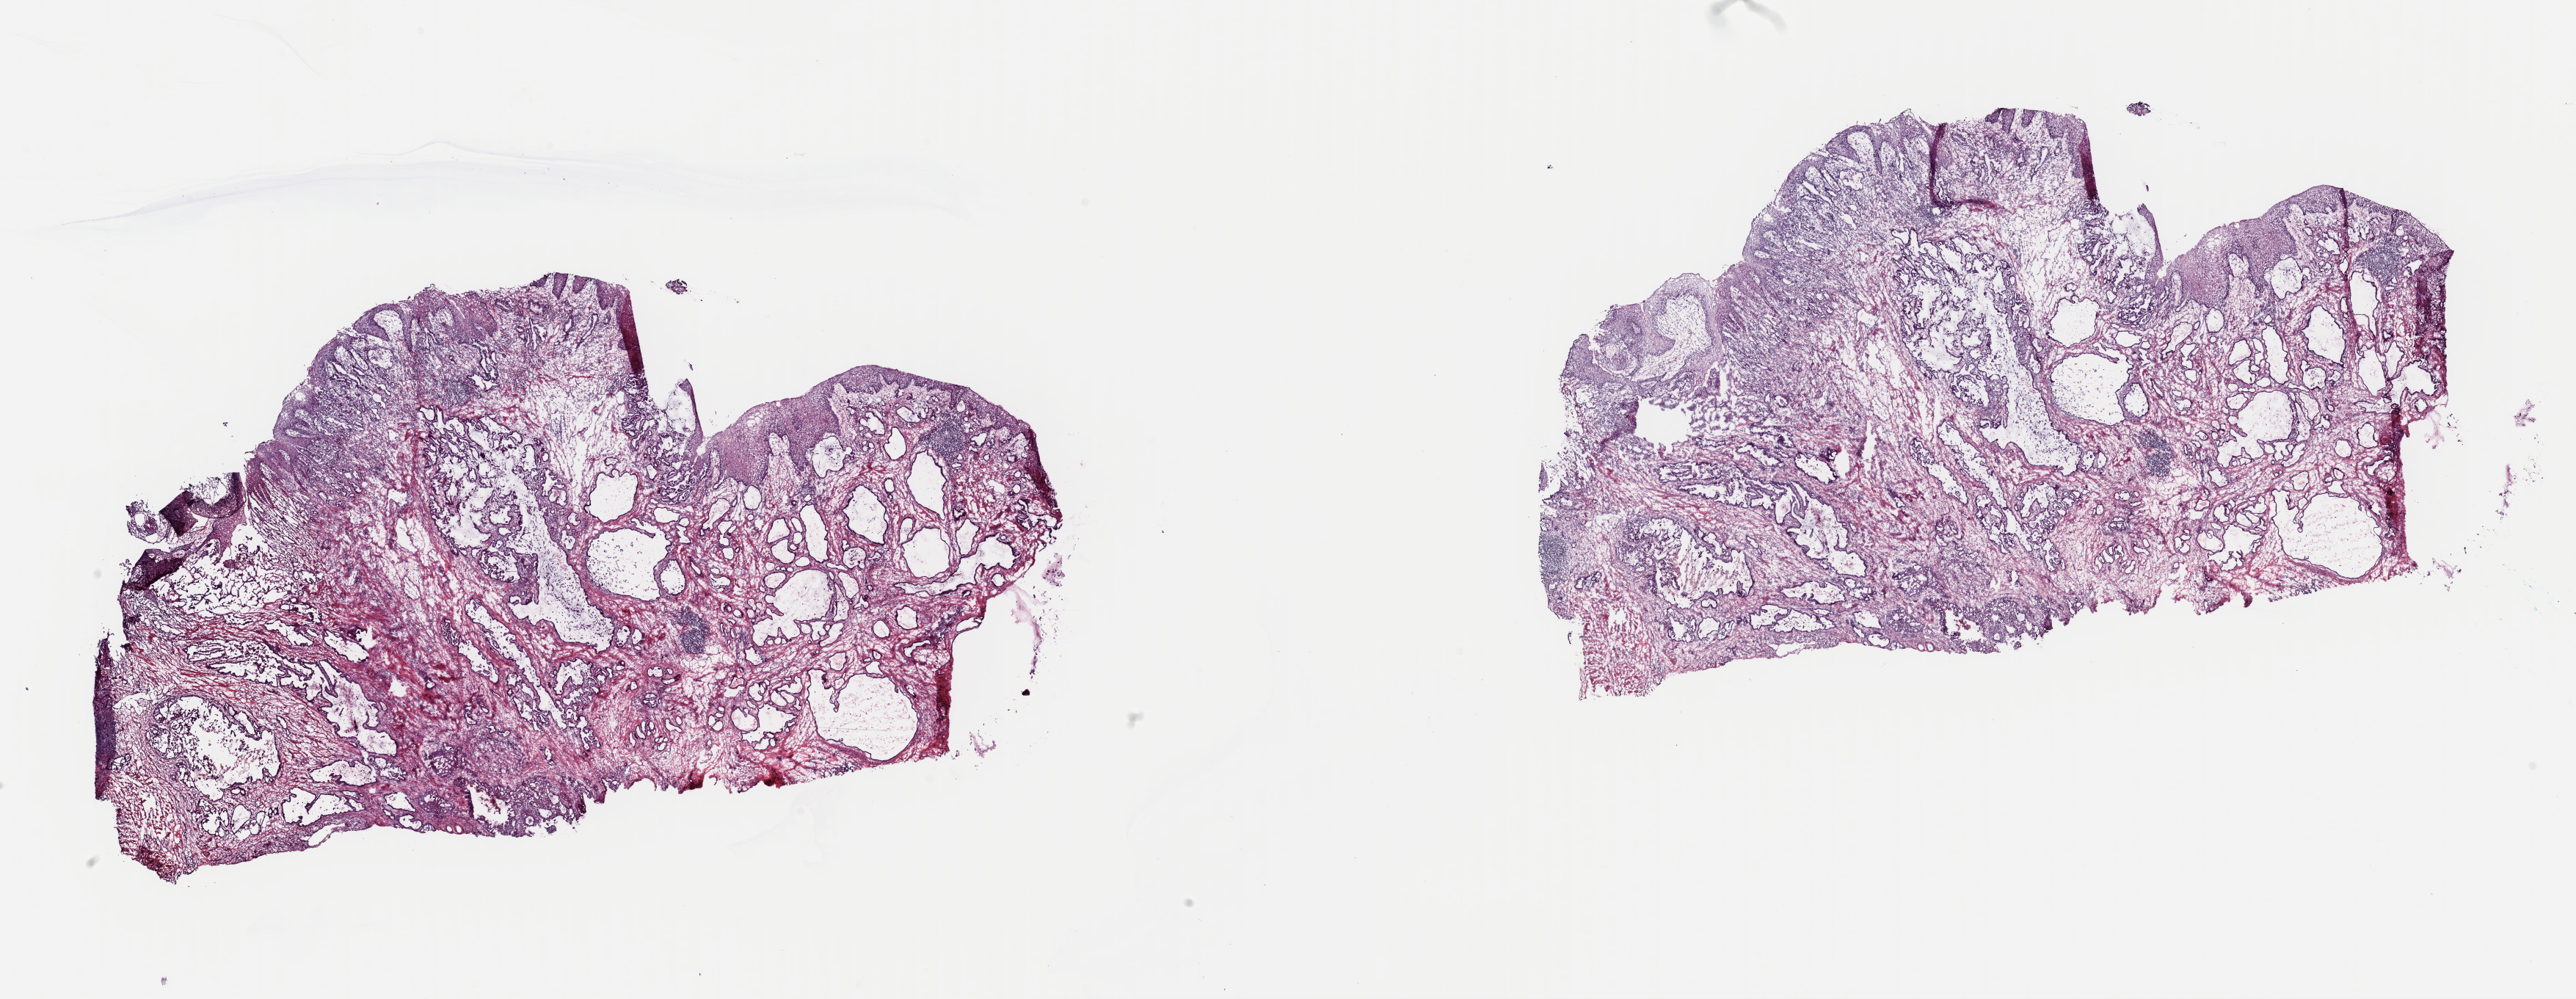
Digitized H&E-stained tissue section (whole slide), a low-resolution overview of the entire scanned area, about 27.7 x 10.8 mm (from a 40x scan), frozen section from the top of the tissue portion, sample: primary tumour, esophagus. Male, age 61 years at initial diagnosis. Histologic grade: G2 (moderately differentiated). Composition of this section per pathologist review: tumour cells 97%, tumour nuclei 60%, normal cells 3%, stromal cells 0%, necrosis 0%. Inflammatory infiltration, as recorded: lymphocyte infiltration 10%, monocyte infiltration 1%, neutrophil infiltration 2%.
• AJCC pathologic stage: IIIB (7th edition)
• histologic diagnosis: Adenocarcinoma, NOS (lower third of esophagus)
• lymph nodes positive (case pathology): 3 of 62 examined